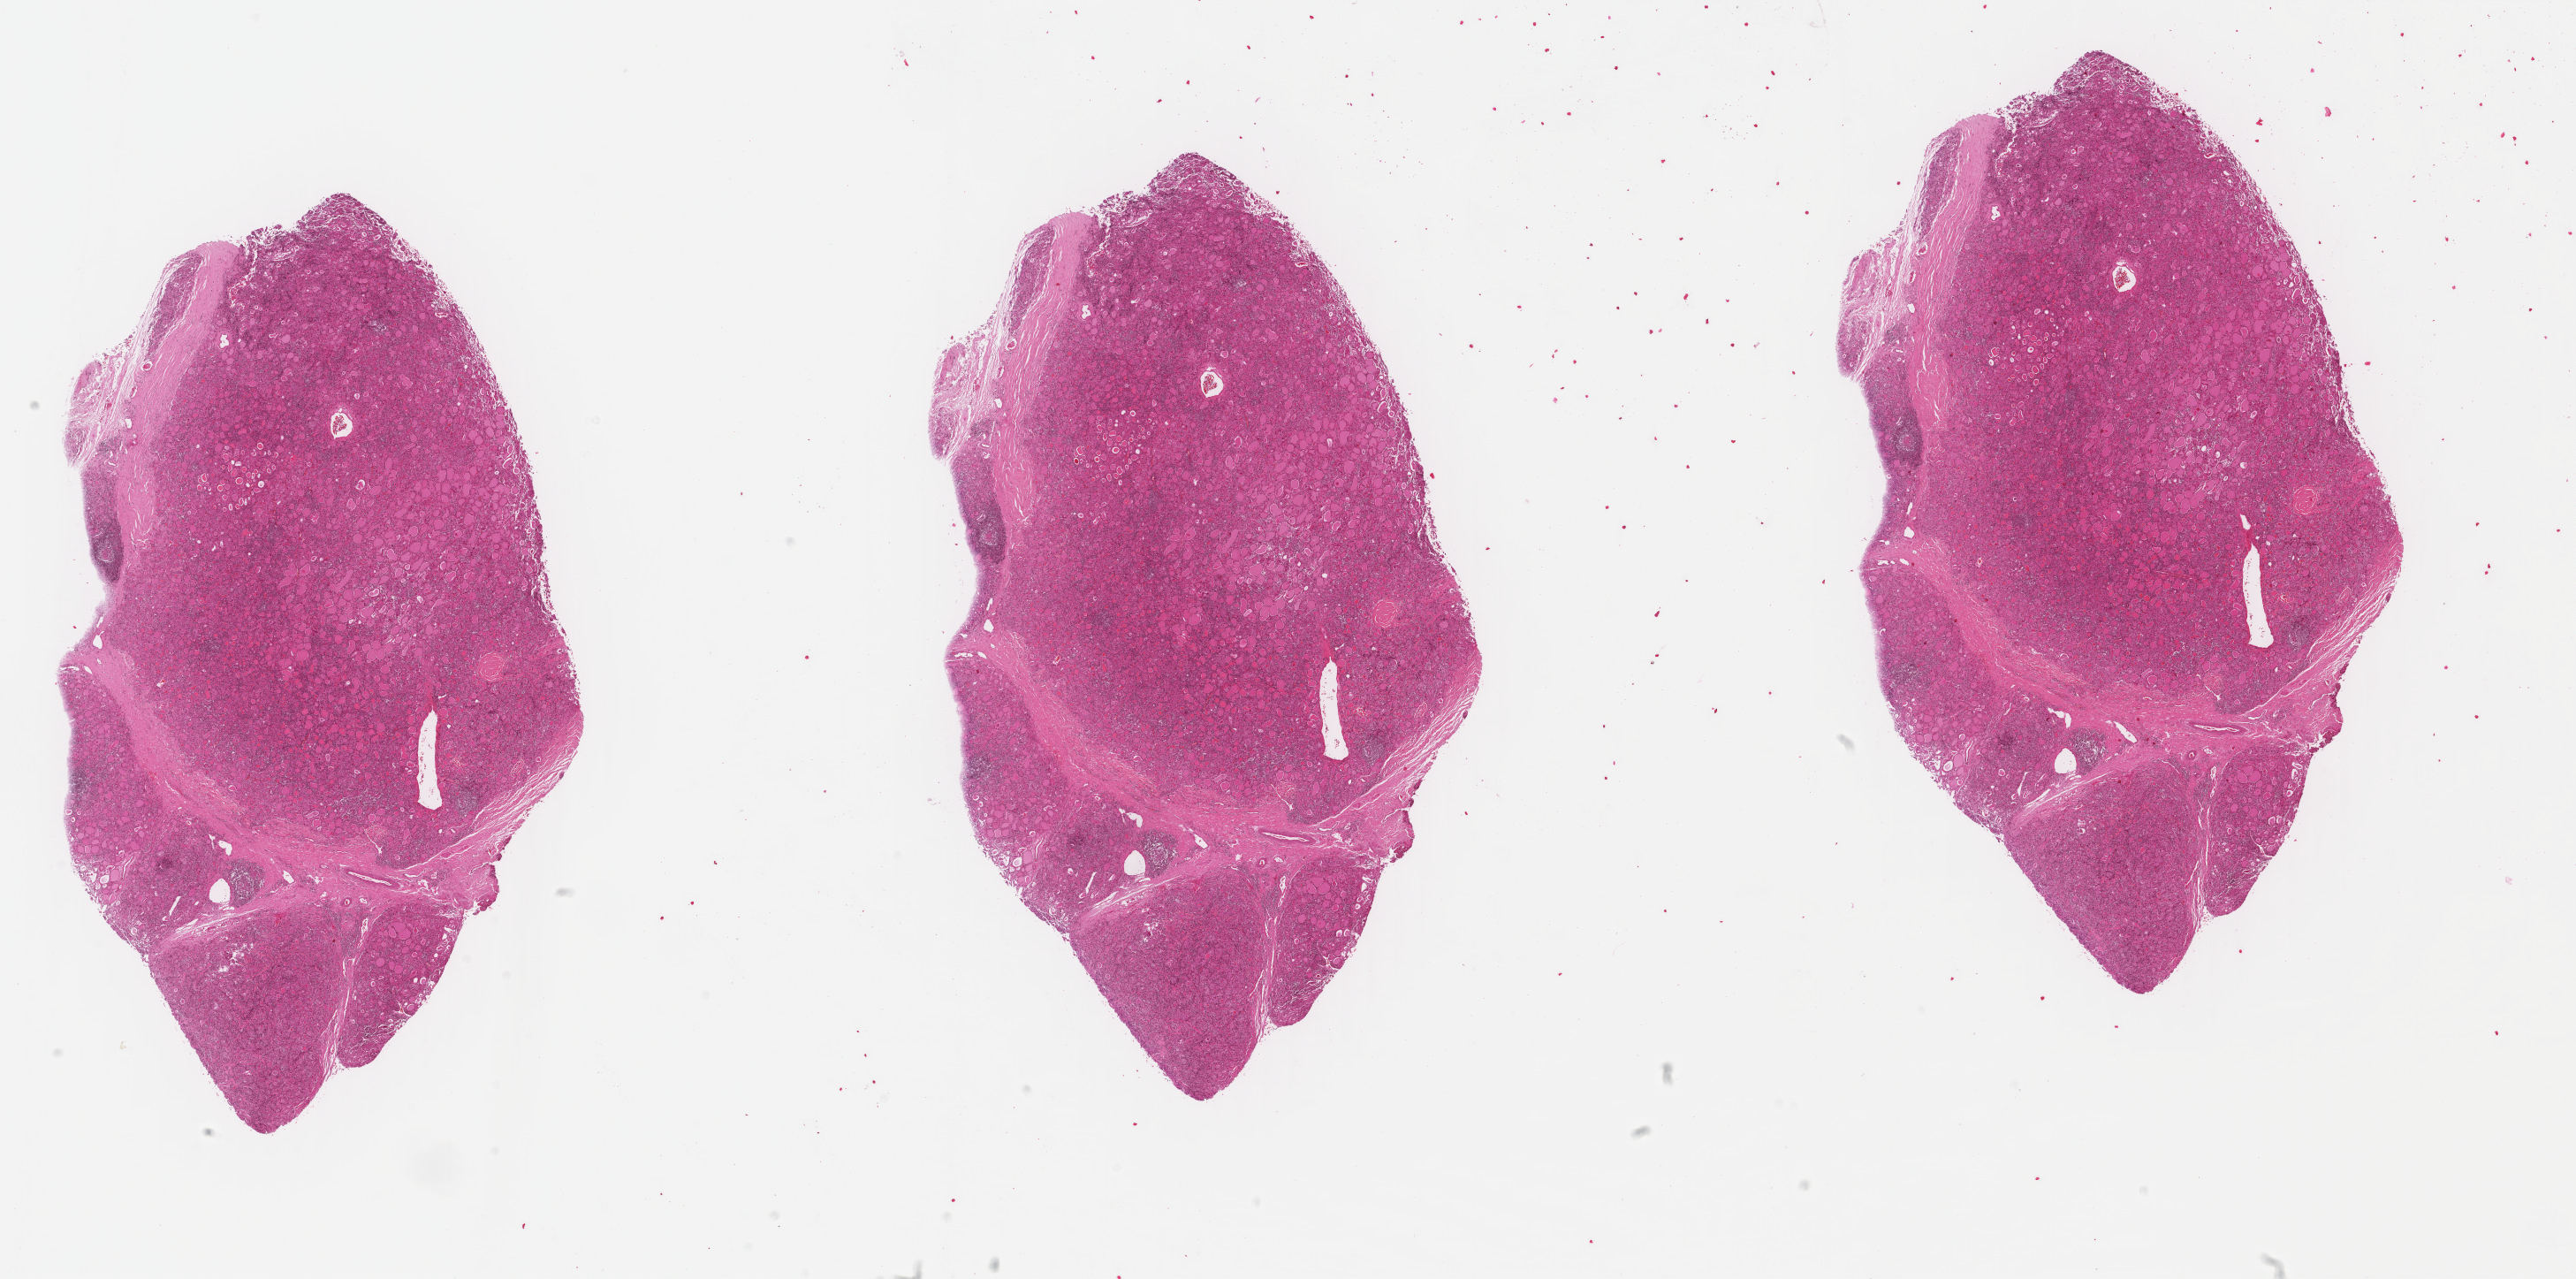
Digitized H&E-stained tissue section (whole slide), shown as a low-resolution overview of the whole scanned area (about 23.1 x 11.5 mm, acquisition: 40x scan). FFPE section. Sample: primary tumour, liver. Male patient; age at initial diagnosis 80 years. Histologic grade: G2 (moderately differentiated).
- diagnosis: Hepatocellular carcinoma, NOS